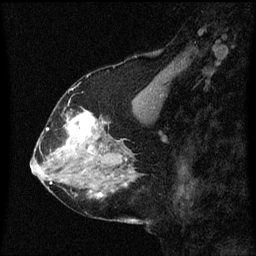
Breast MRI (dynamic contrast-enhanced), one sagittal slice; position 26 of 60 along the scan axis; dynamic contrast-enhanced series, image 2 of 3 at this slice position (ordered by acquisition); 1.5 T; TE 4.2 ms, TR 8.4 ms; 2 mm slice thickness; 256 × 256 image matrix, field of view 200 × 200 mm. Patient: female, 58 years.
Annotated regions visible in this slice (semi-automatic segmentation, software-assisted and operator-edited):
- analysis volume of interest (the breast-tissue region the enhancement analysis was run in; not a lesion): bounding box <58,108,99,151> (left, top, right, bottom; pixels)
- tumour enhancement mask (voxels above the 70 % enhancement threshold inside the analysis volume of interest): <62,112,97,151>